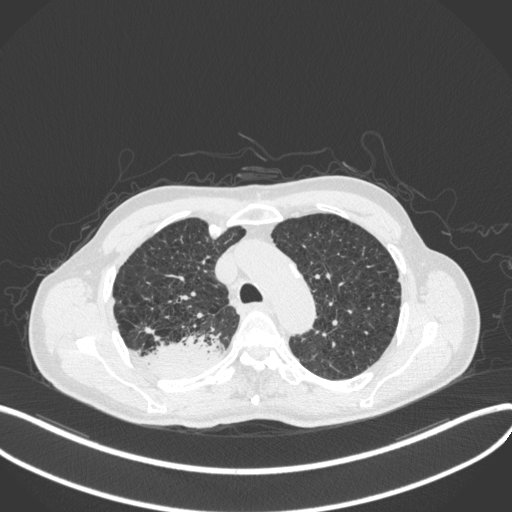
Chest CT, one axial slice. Position 332 of 423 along the scan axis. 120 kVp. Lung window (W 1500 / L -600 HU). 512 × 512 image matrix, field of view 400 × 400 mm. Patient: male, 79 years. From the clinical record (not read from this slice): clinical TNM (as recorded): T3 N0 M0.
Outlined on this slice (rectangle marked by the reading radiologist):
- lung tumour (recorded histology: adenocarcinoma): bounding box (x1, y1, x2, y2) in pixels: (145, 332, 229, 379)